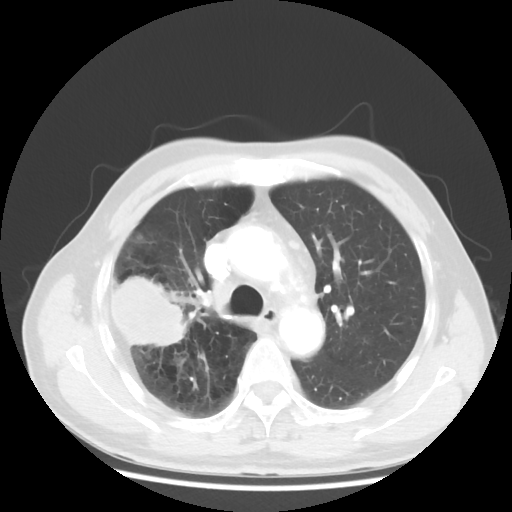
Chest CT, one axial slice; slice 34 of 50 in the series (ordered by position); 120 kVp; lung window (W 1500 / L -600 HU); 512 × 512 image matrix, field of view 360 × 360 mm. Male patient, age 69 years. Case-level facts recorded for this patient, not image findings: clinical TNM (as recorded): T3 N0 M0.
Outlined on this slice (bounding box drawn by a radiologist):
- lung tumour (recorded histology: adenocarcinoma): bounding box (x1, y1, x2, y2) in pixels: (109, 269, 191, 350)